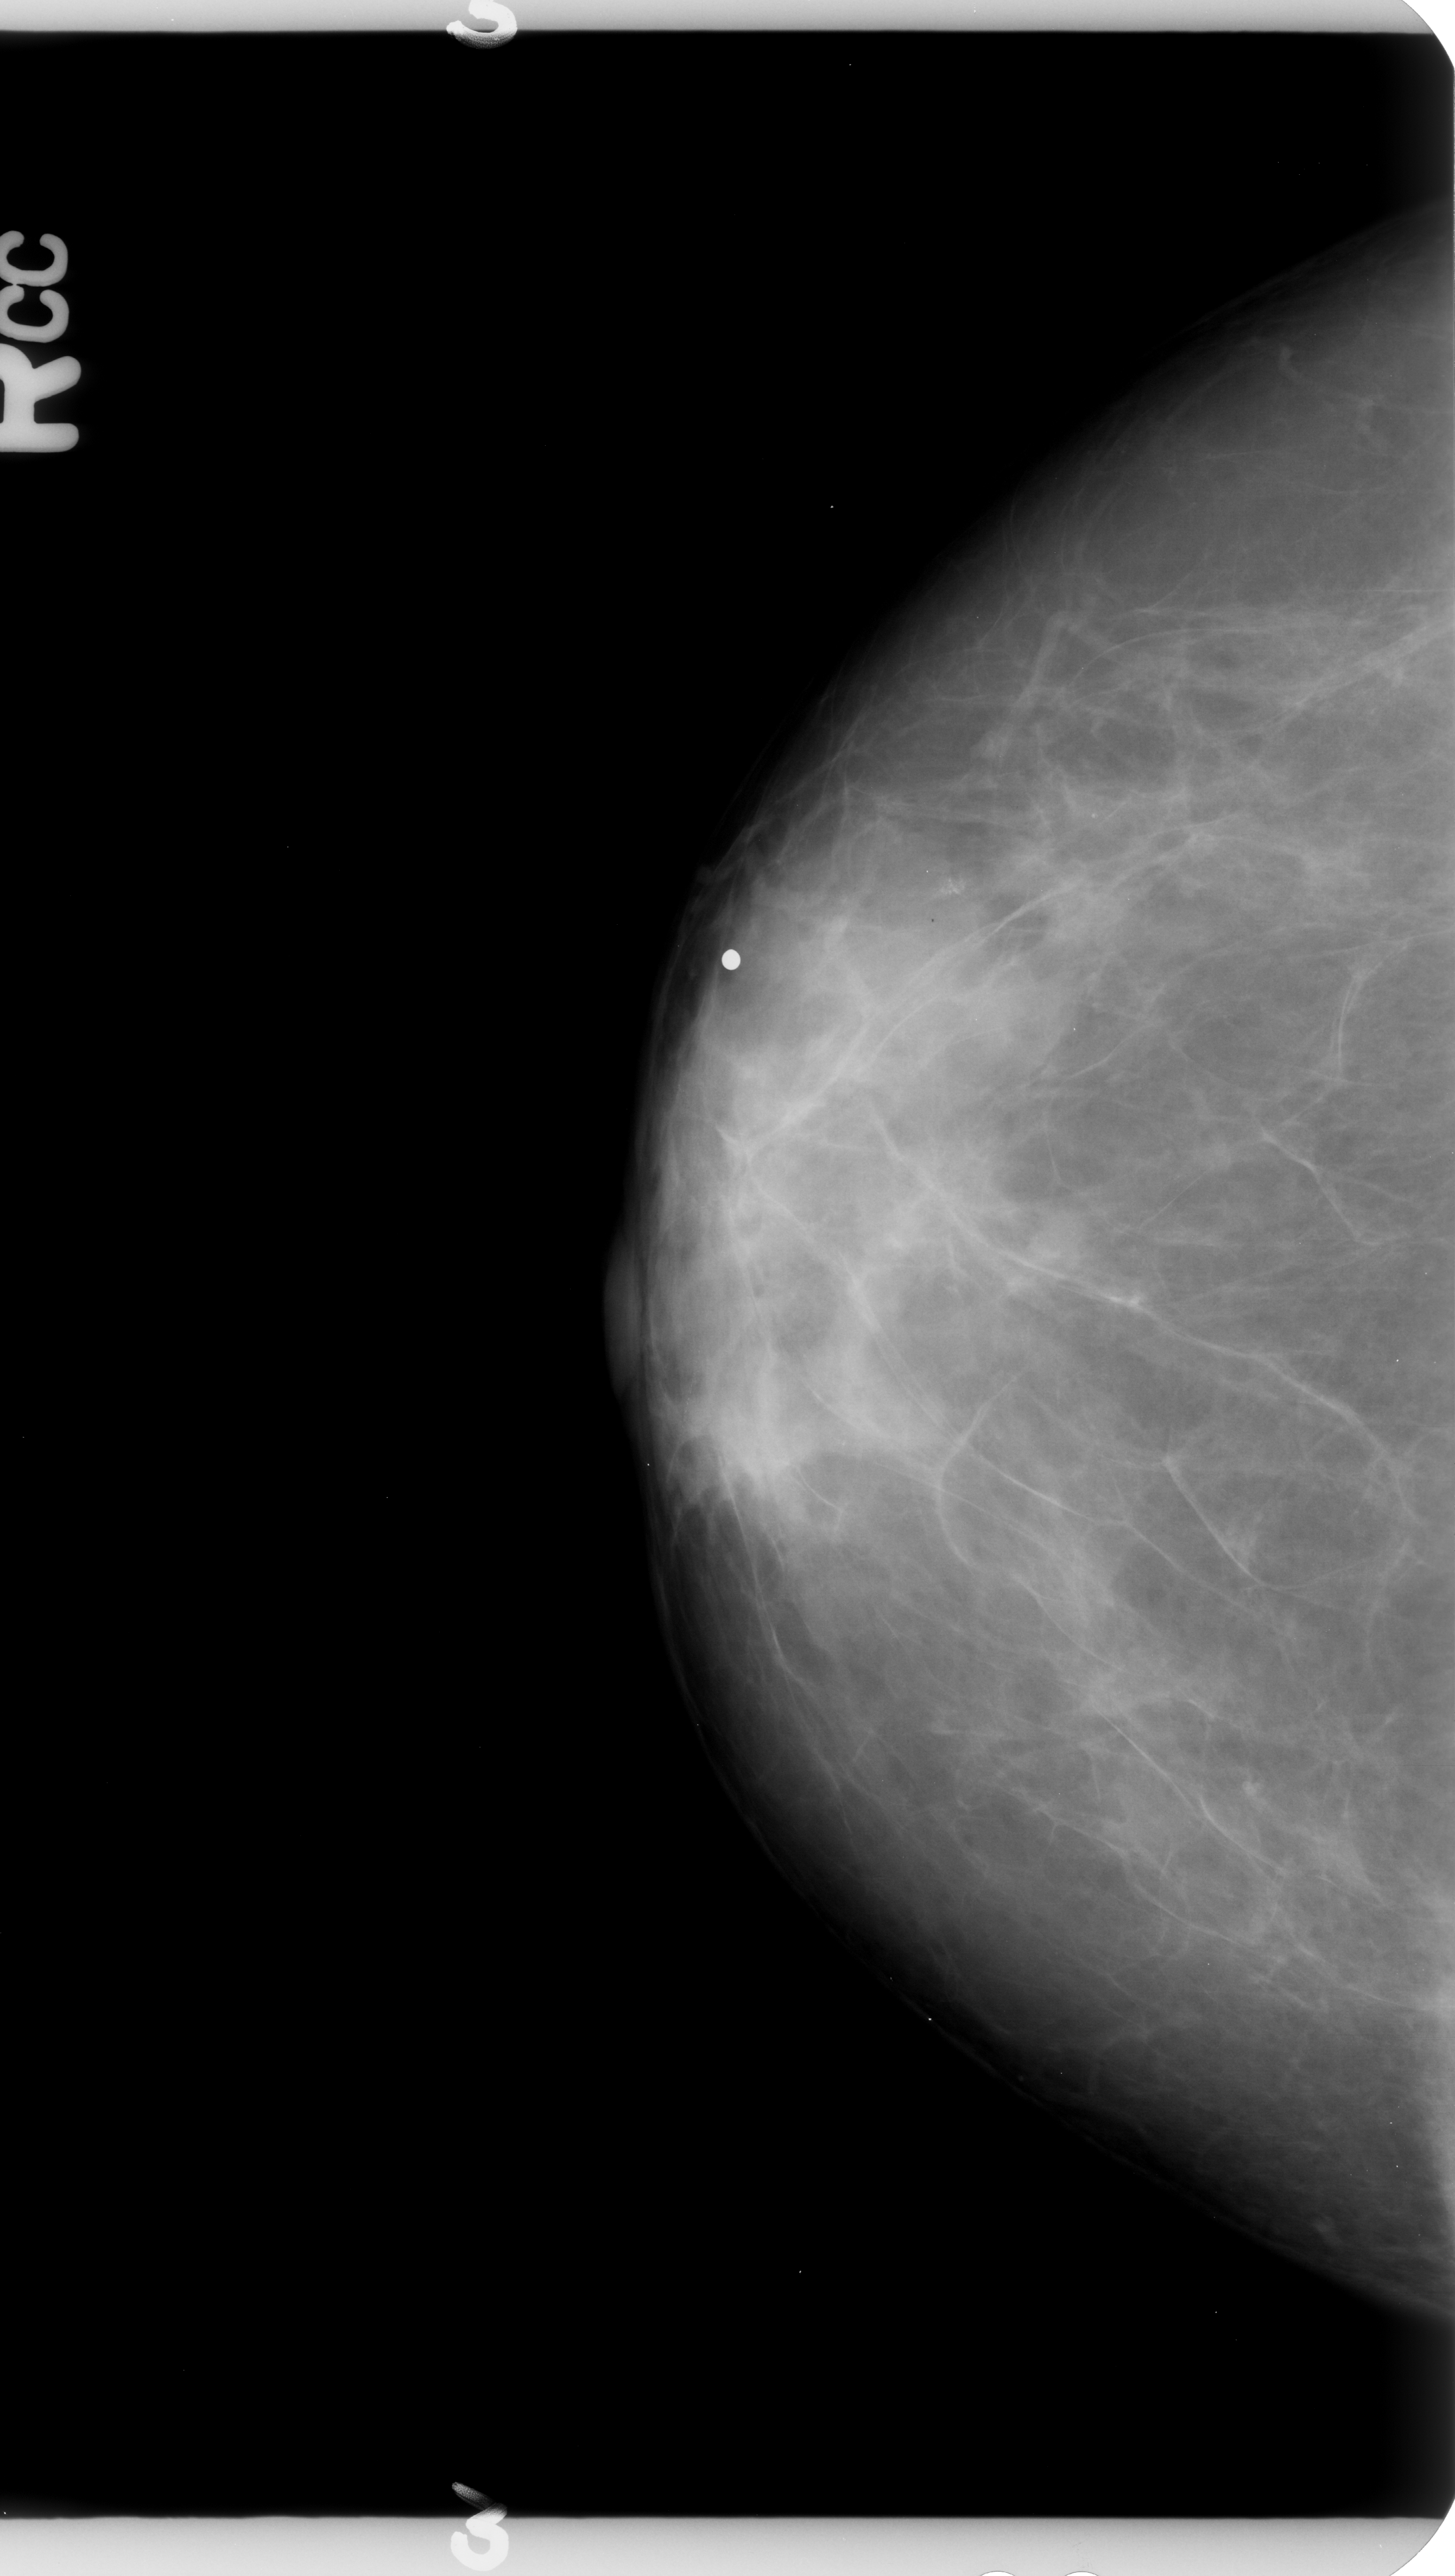
Mammogram (digitized film), right breast, craniocaudal (CC) view, breast composition: heterogeneously dense (BI-RADS density category 3 of 4).
Calcifications, morphology pleomorphic, distribution clustered; BI-RADS assessment category 4; subtlety rating 3 on a 1 (subtle) to 5 (obvious) scale; pathology result (as recorded, not read from the image): benign.